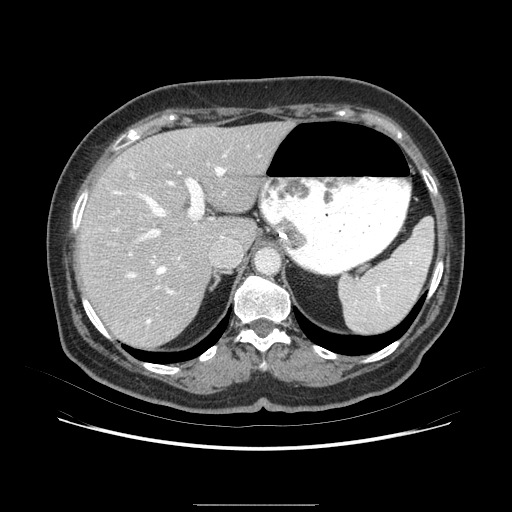
Contrast-enhanced abdominal CT (liver protocol), one axial slice; position 53 of 79 along the scan axis; 120 kVp; soft-tissue window (W 400 / L 40 HU); 2.5 mm slice thickness; 512 × 512 image matrix, field of view 380 × 380 mm. Case-level facts recorded for this patient, not image findings: diagnosis: hepatocellular carcinoma (patient treated with transarterial chemoembolisation; whether this scan precedes or follows treatment is not stated here); TNM stage (as recorded): Stage-I; Child-Pugh class: A.
Annotated regions visible in this slice (semi-automatic segmentation, software-assisted and operator-edited):
- abdominal aorta: bounding box [x1, y1, x2, y2] px = [257, 249, 282, 277]
- liver parenchyma outside the tumour (the mass and vessels are separate outlines, so this box may not span the whole liver): [76, 126, 298, 342]
- liver vessels: [116, 159, 234, 326]